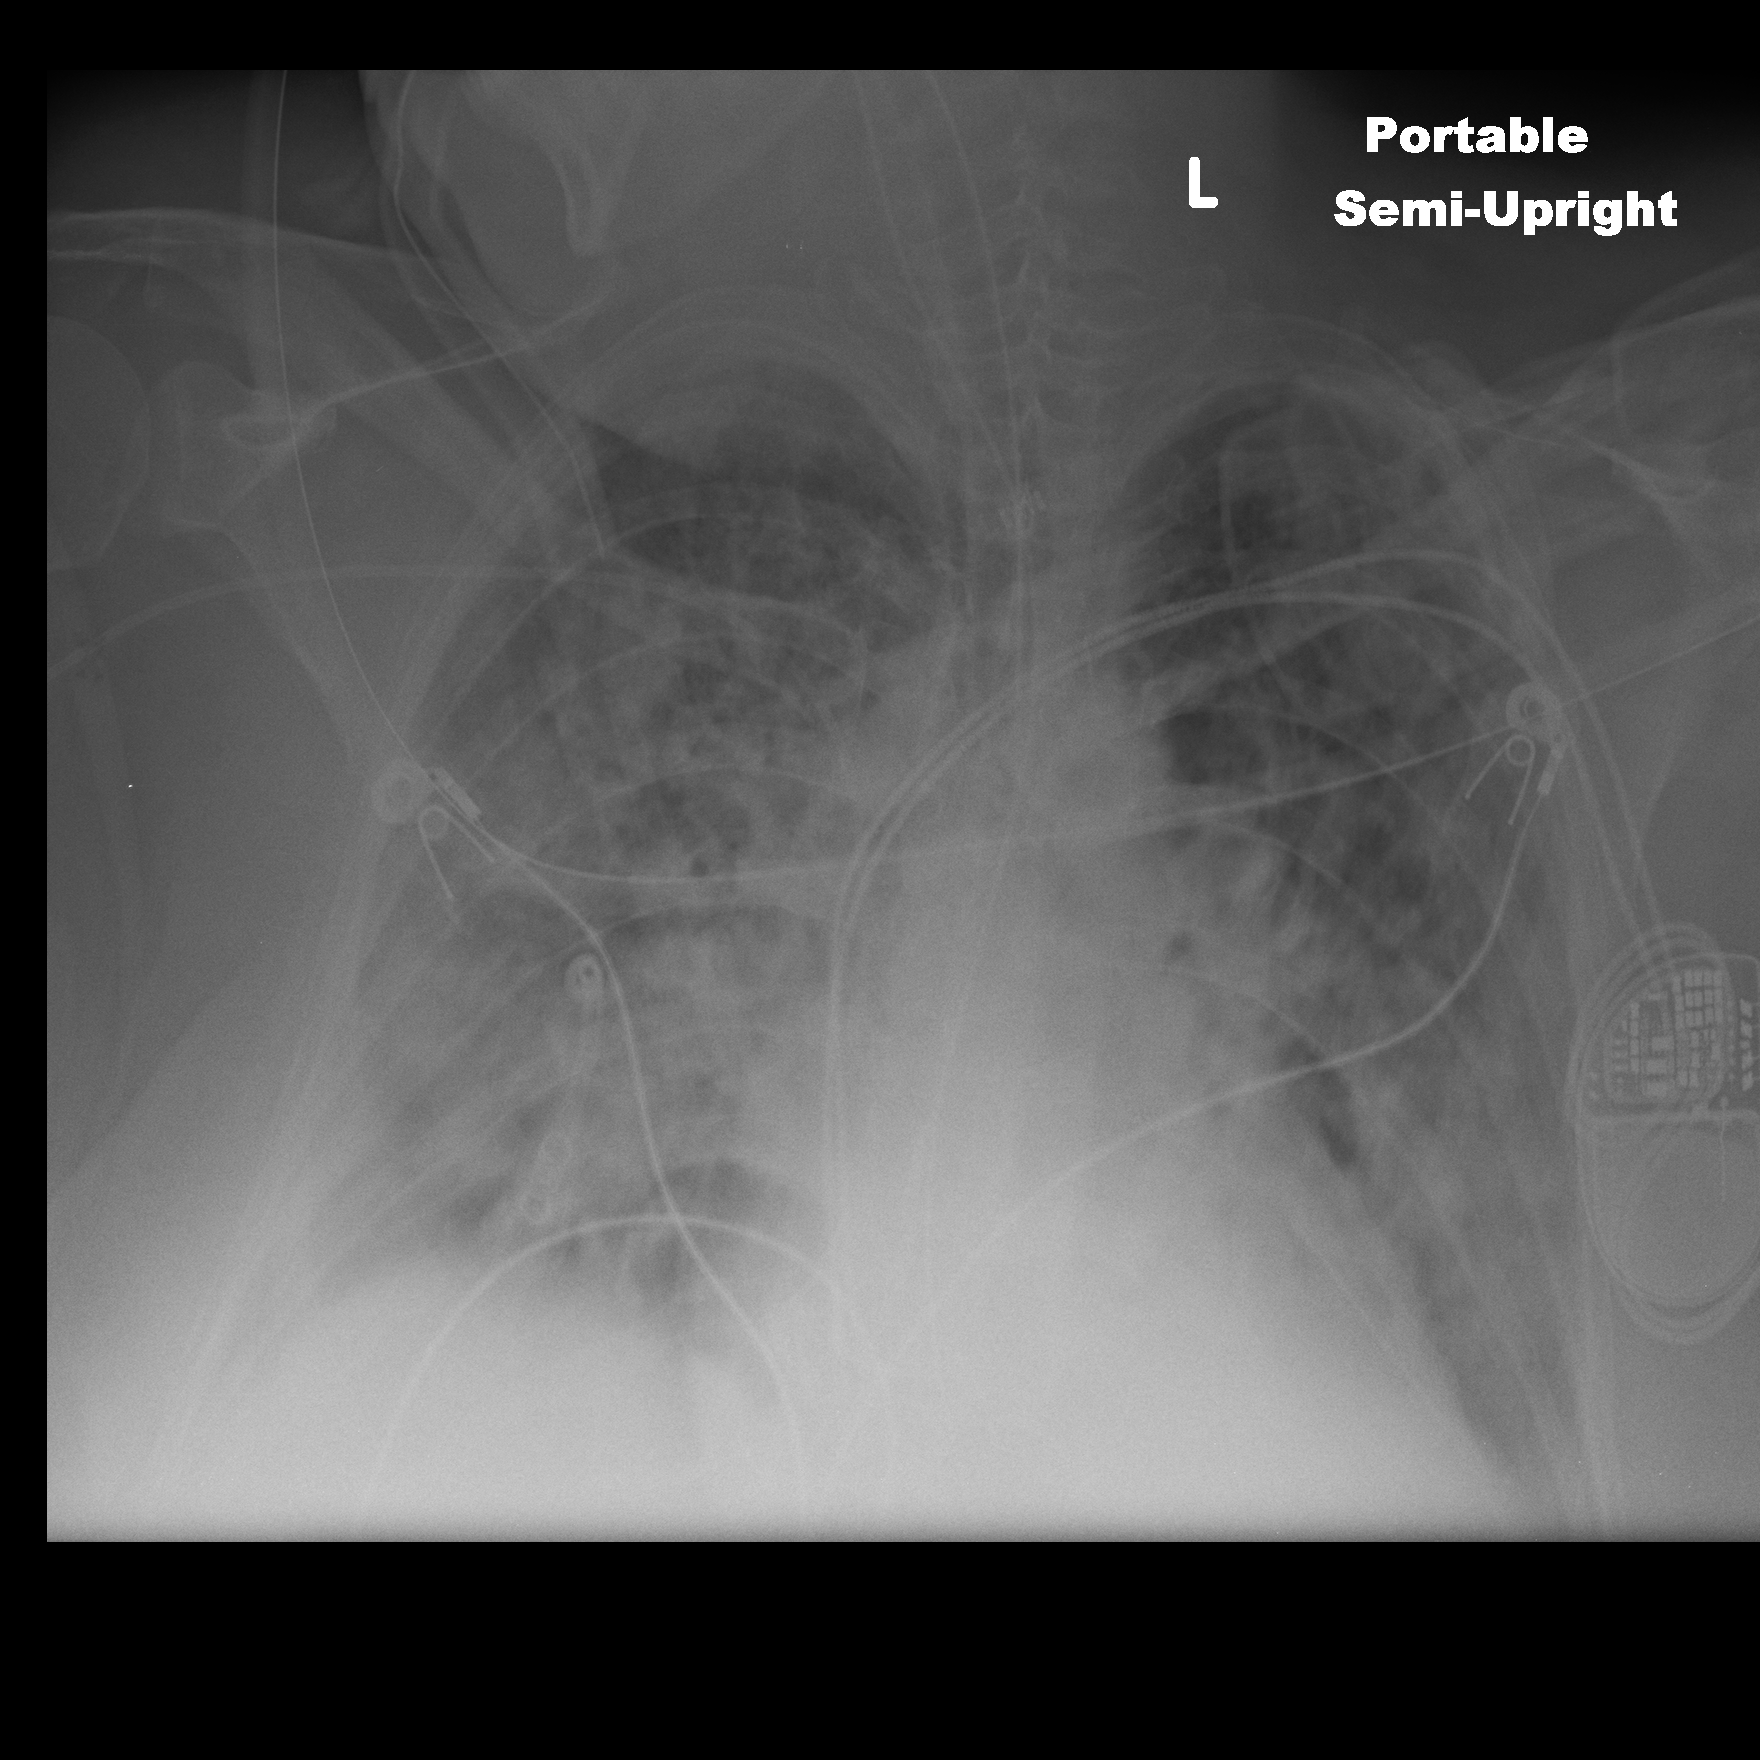
Chest X-ray (portable), AP projection. Female patient, age 57 years; imaged 2 days after the COVID-19 diagnosis.
Key findings recorded by the radiologist: Worsening diffuse airspace disease noted throughout the lungs.